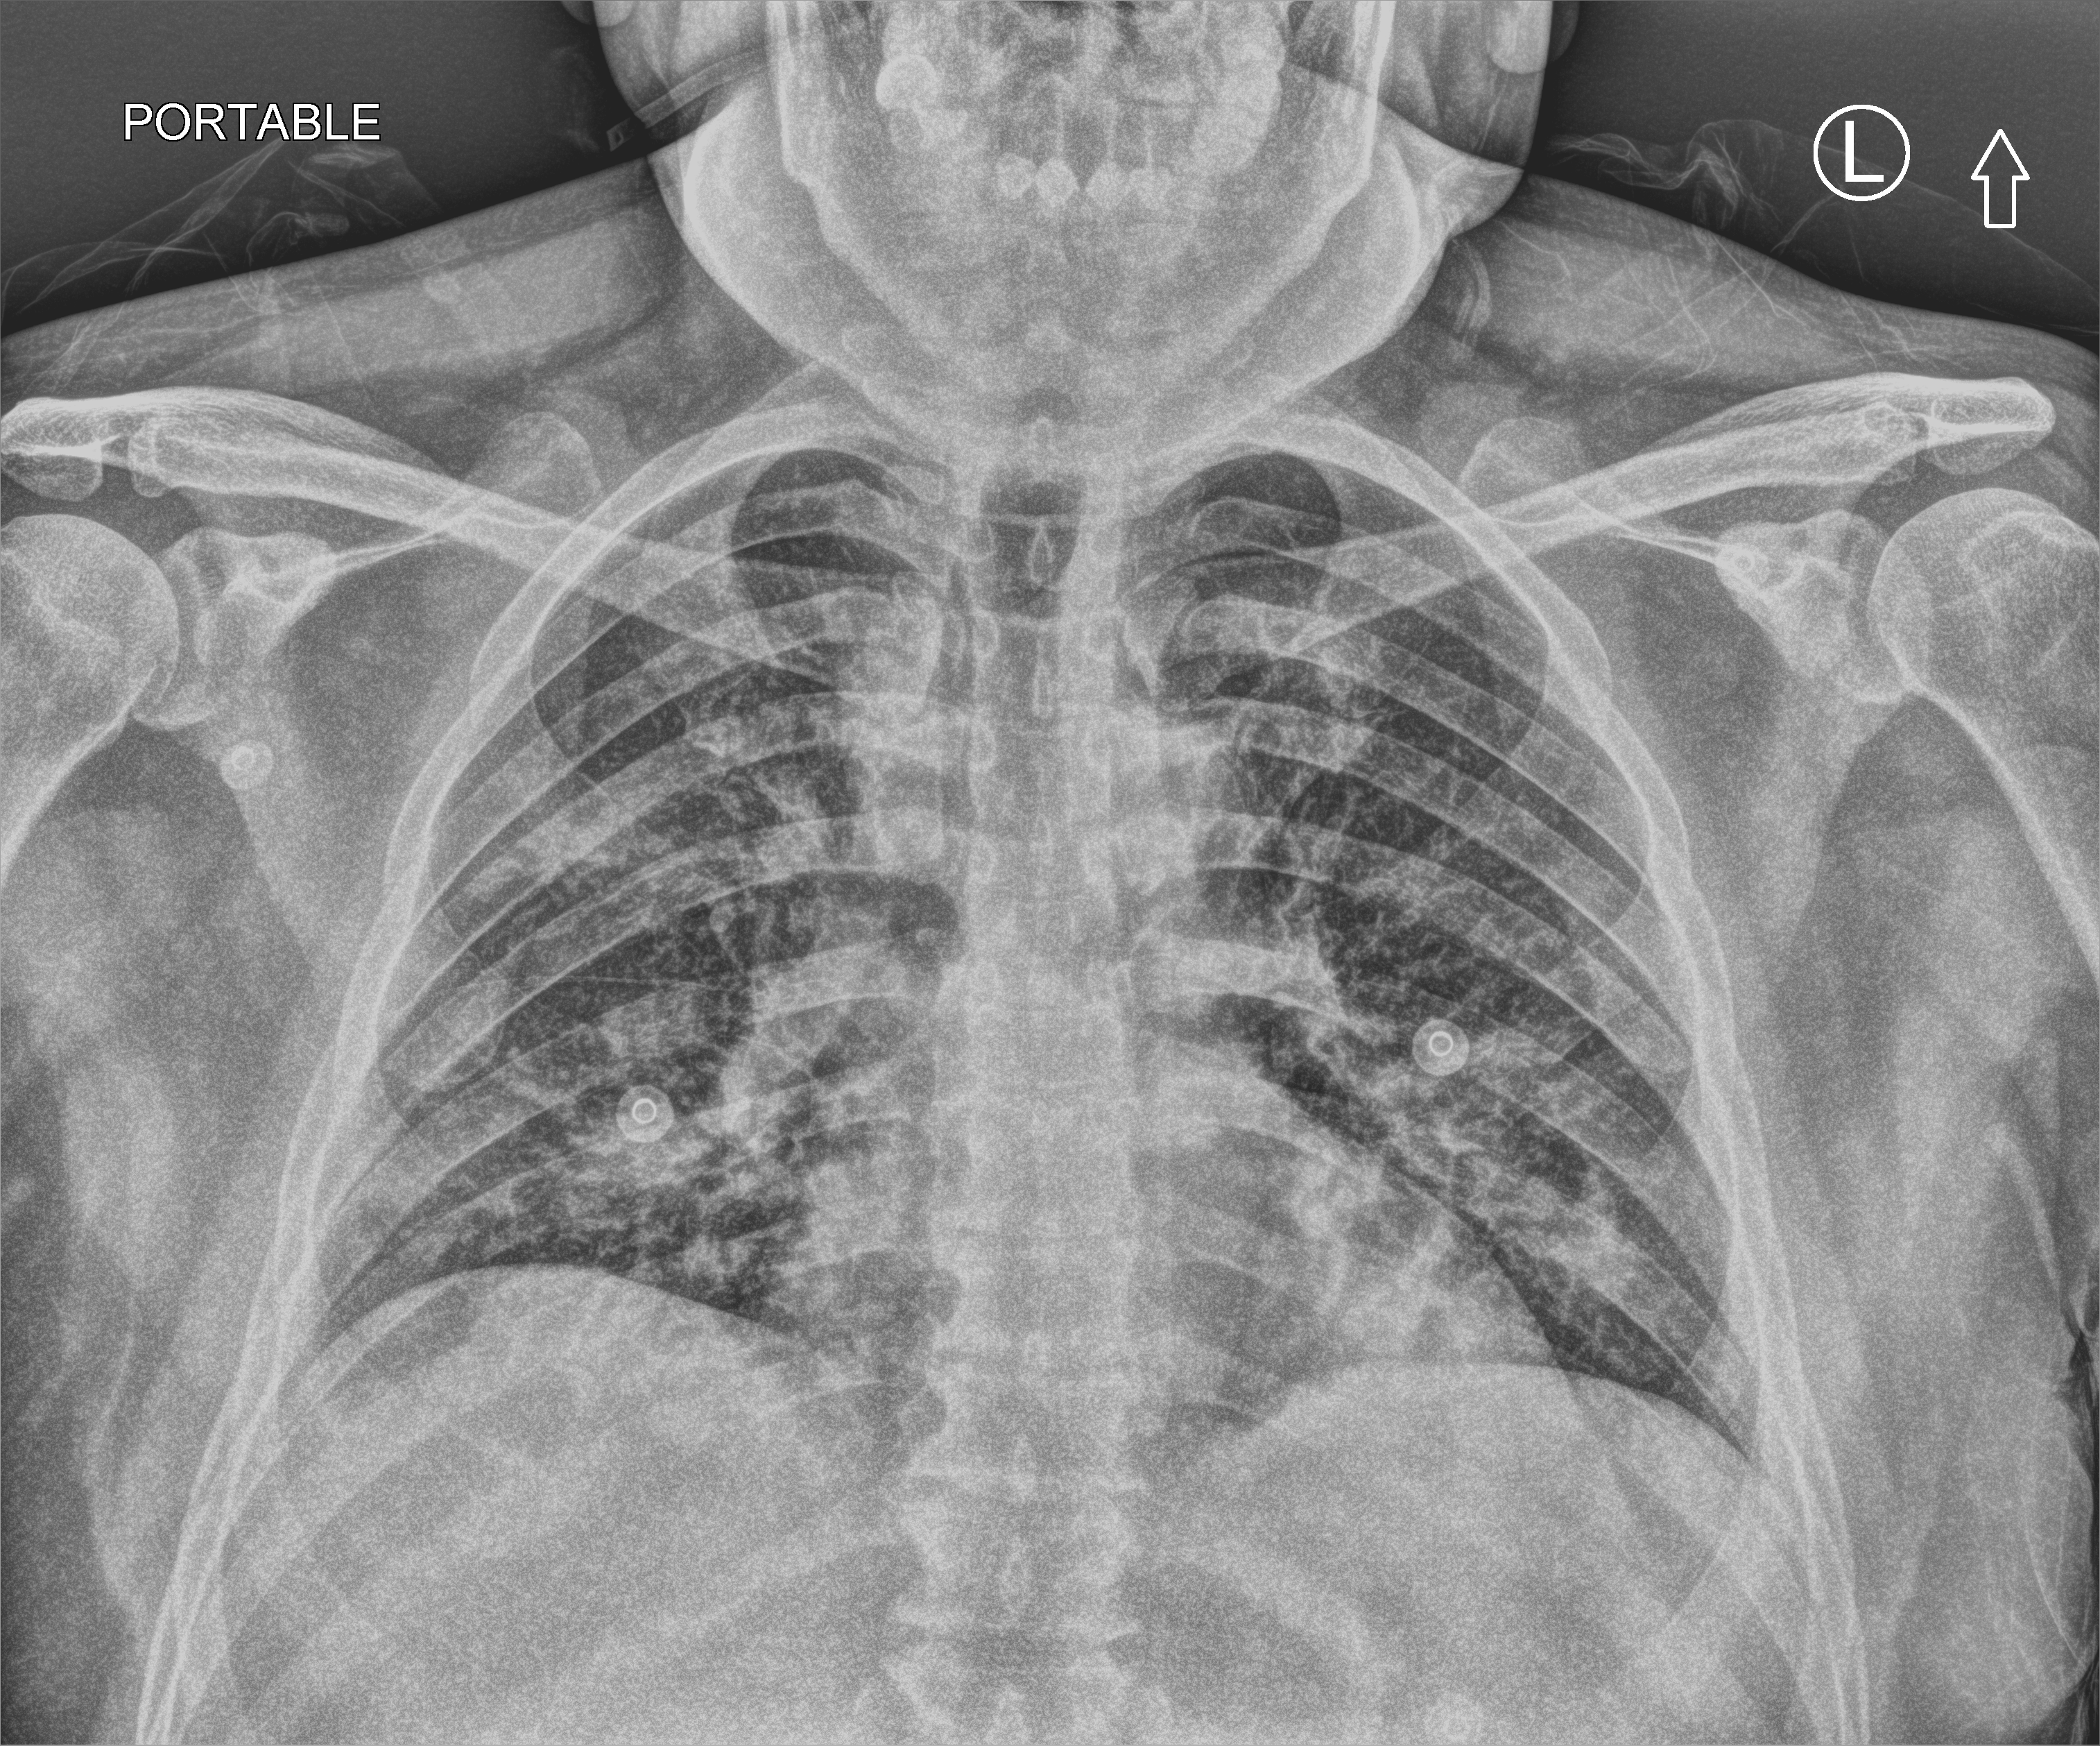
Bedside chest radiograph (computed radiography). Patient hospitalised with COVID-19; male, aged 18–59 years.
From the hospital-stay record, not from the radiograph (when in the stay this image was taken is not recorded): COPD (admission record): no; admitted to intensive care during this hospital stay: no.